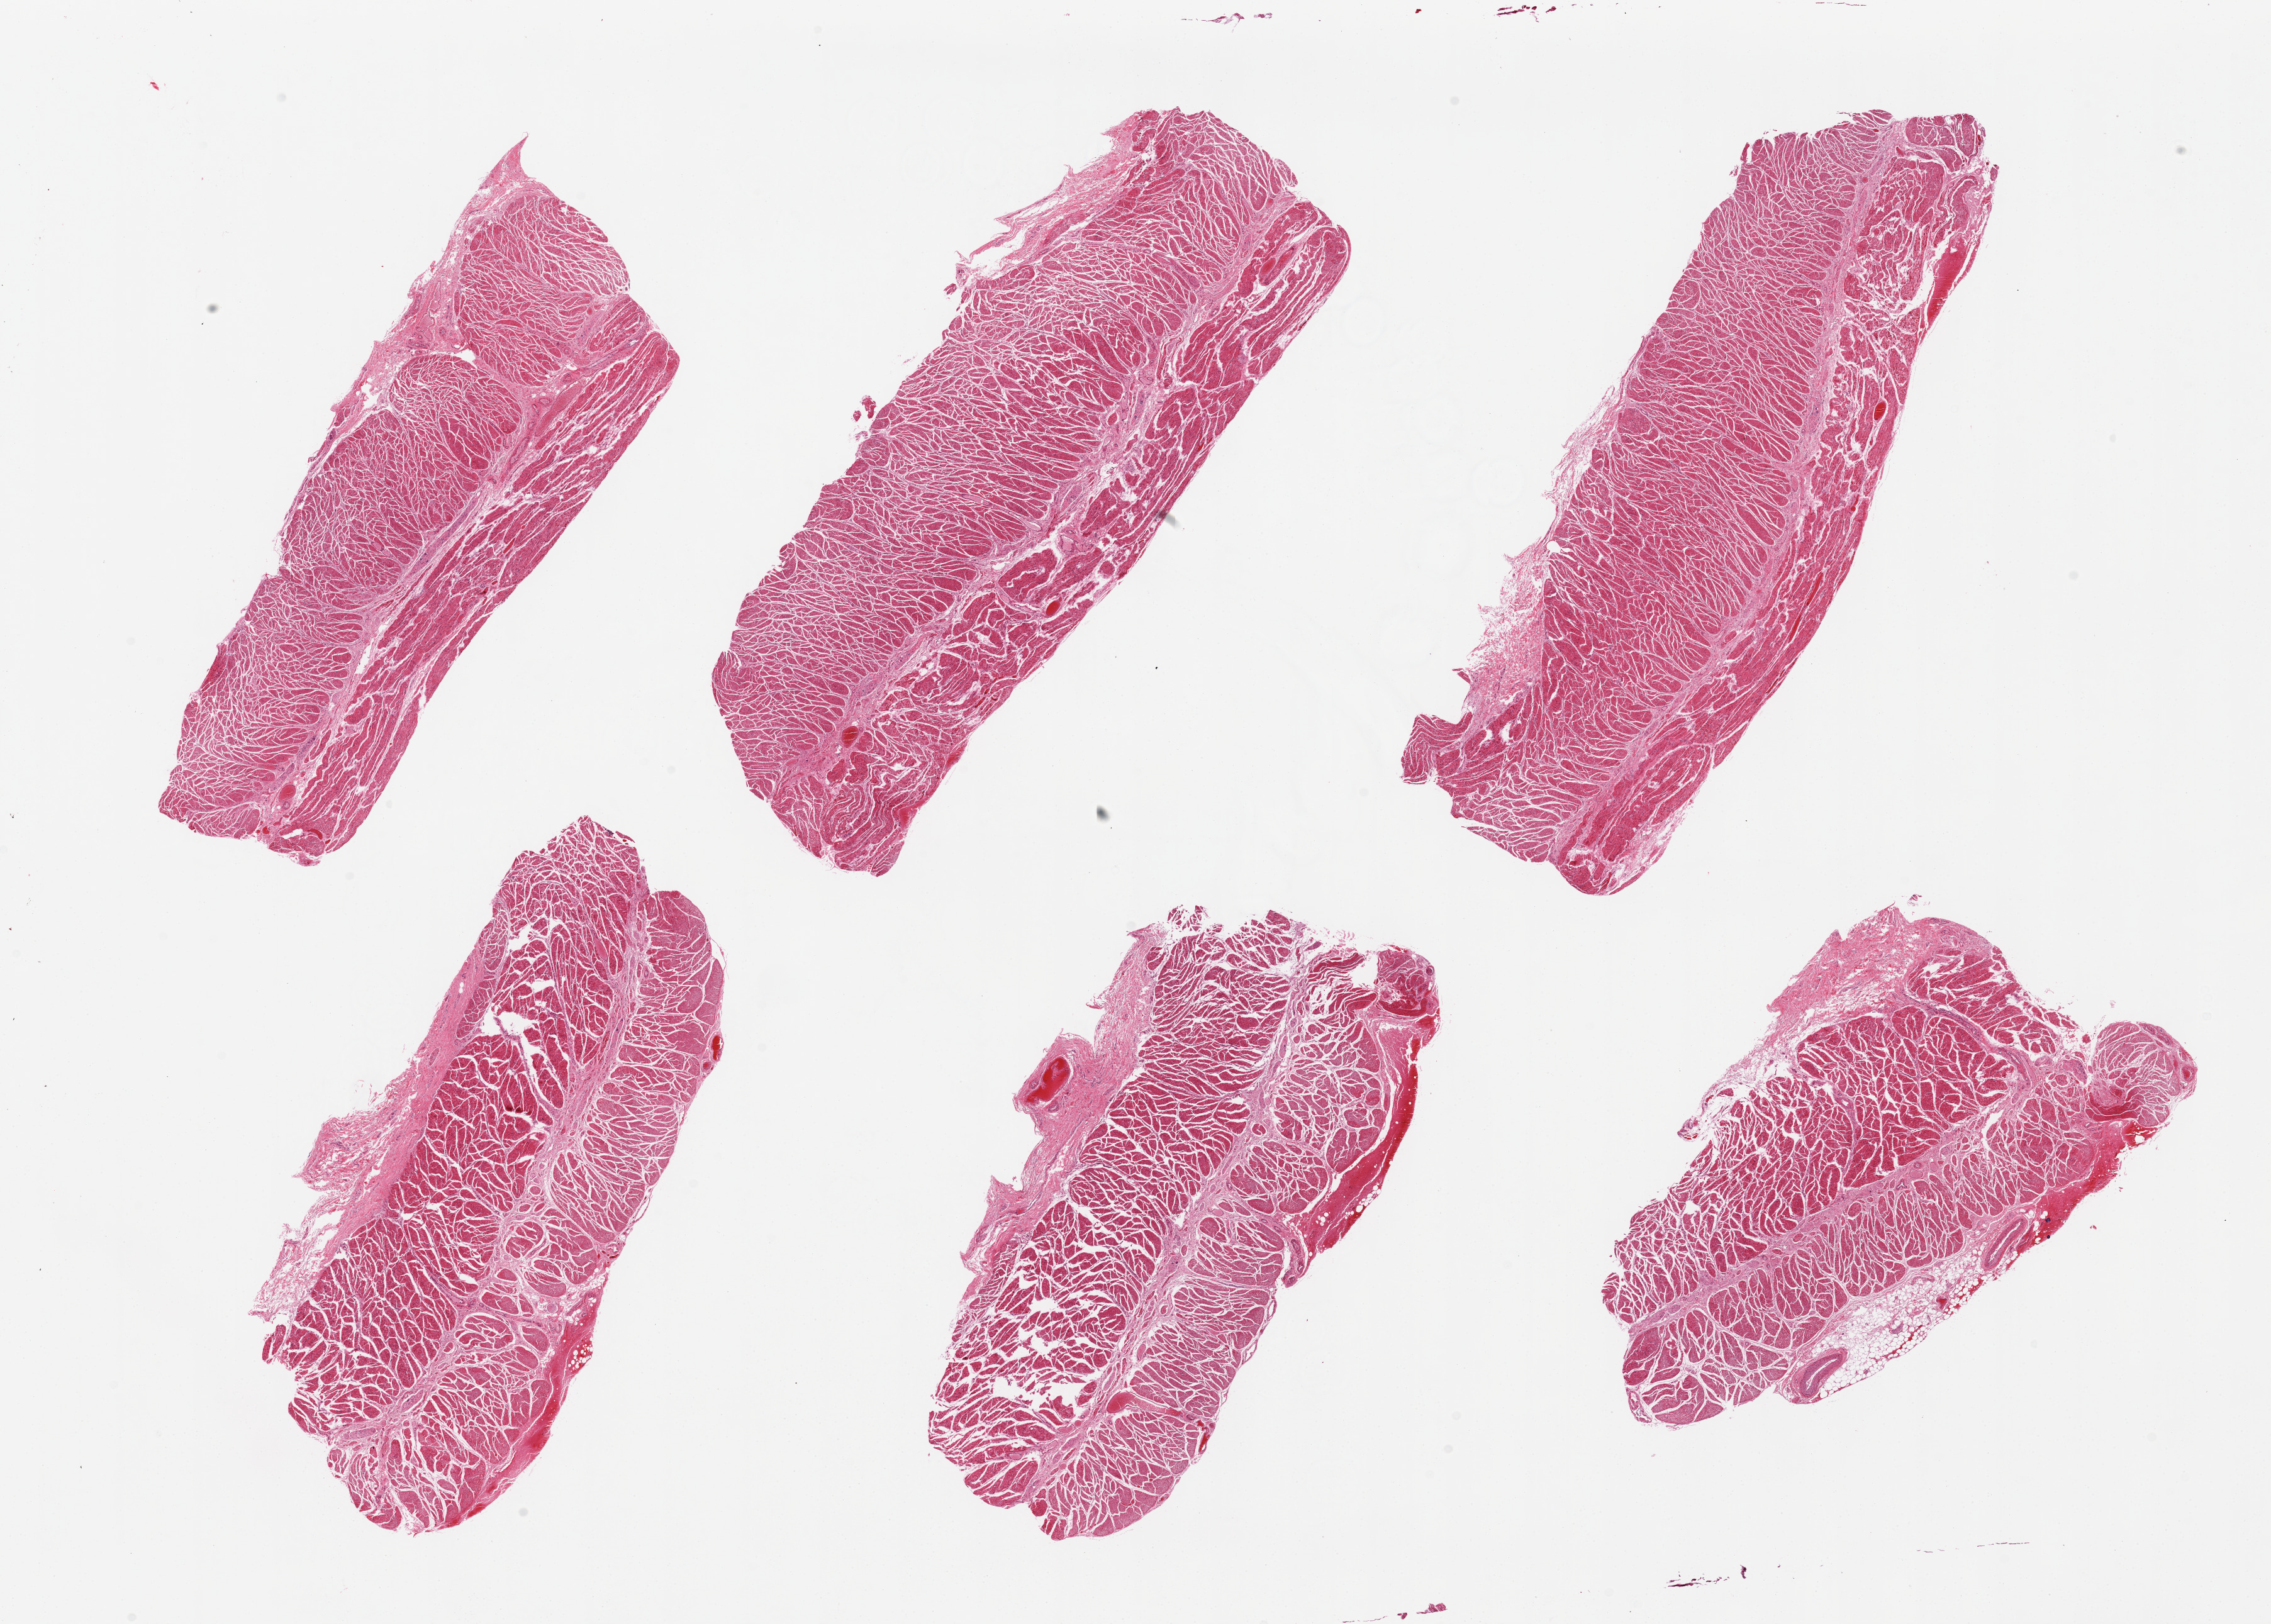
Hematoxylin and eosin (H&E) whole-slide image, shown as a low-resolution overview of the whole scanned area (about 28.5 x 20.4 mm, acquisition: 20x scan); PAXgene-fixed, paraffin-embedded tissue; target tissue: esophageal muscle; donor tissue sample. Donor sex: male.
• review note (as recorded): 6 pieces, all muscularis